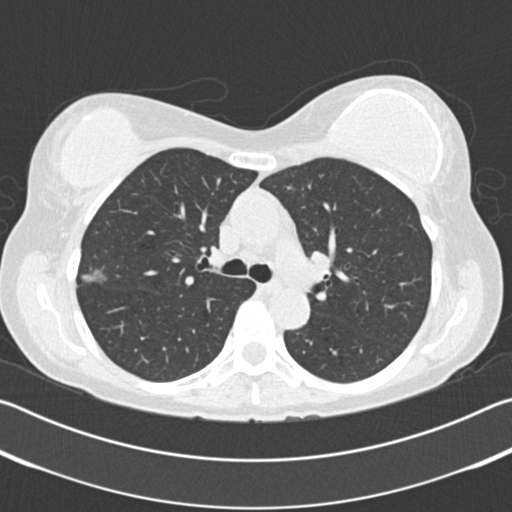
Low-dose screening chest CT, axial slice; second screening round (one year after baseline); lung window (W 1500 / L -600 HU); 2 mm slice thickness; standard (soft-tissue) reconstruction kernel (B30f). Female, age 58 years at enrolment. Former smoker at enrolment.
• Expert reader's lesion annotation, bounding box <63,257,119,303> (left, top, right, bottom; pixels).
• Reader record for this screening exam (exam-level; its link to the box is not recorded): non-calcified nodule or mass ≥4 mm, right upper lobe, 15 × 13 mm, poorly defined margins, ground glass attenuation, pre-existing on the prior screen: no.
• Official screen result: positive, change unspecified: nodule(s) >= 4 mm or enlarging nodule(s), mass(es), or other non-specific abnormalities suspicious for lung cancer.